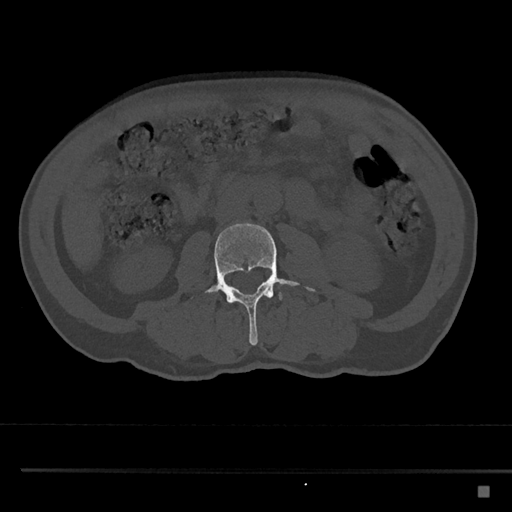
CT including the spine, one axial slice; slice 693 of 797 in the series (ordered by position); reconstruction kernel Br40s/3; bone window (W 1800 / L 400 HU); 0.5 mm slice thickness; 512 × 512 image matrix, field of view 391 × 391 mm. Patient: male, 59 years. From the clinical record (not read from this slice): primary cancer: prostate.
Structures marked on this image (semi-automatically segmented with operator editing):
- L3 vertebra: bounding box [x1, y1, x2, y2] px = [207, 223, 315, 345]
- L4 vertebra: [279, 292, 283, 301]